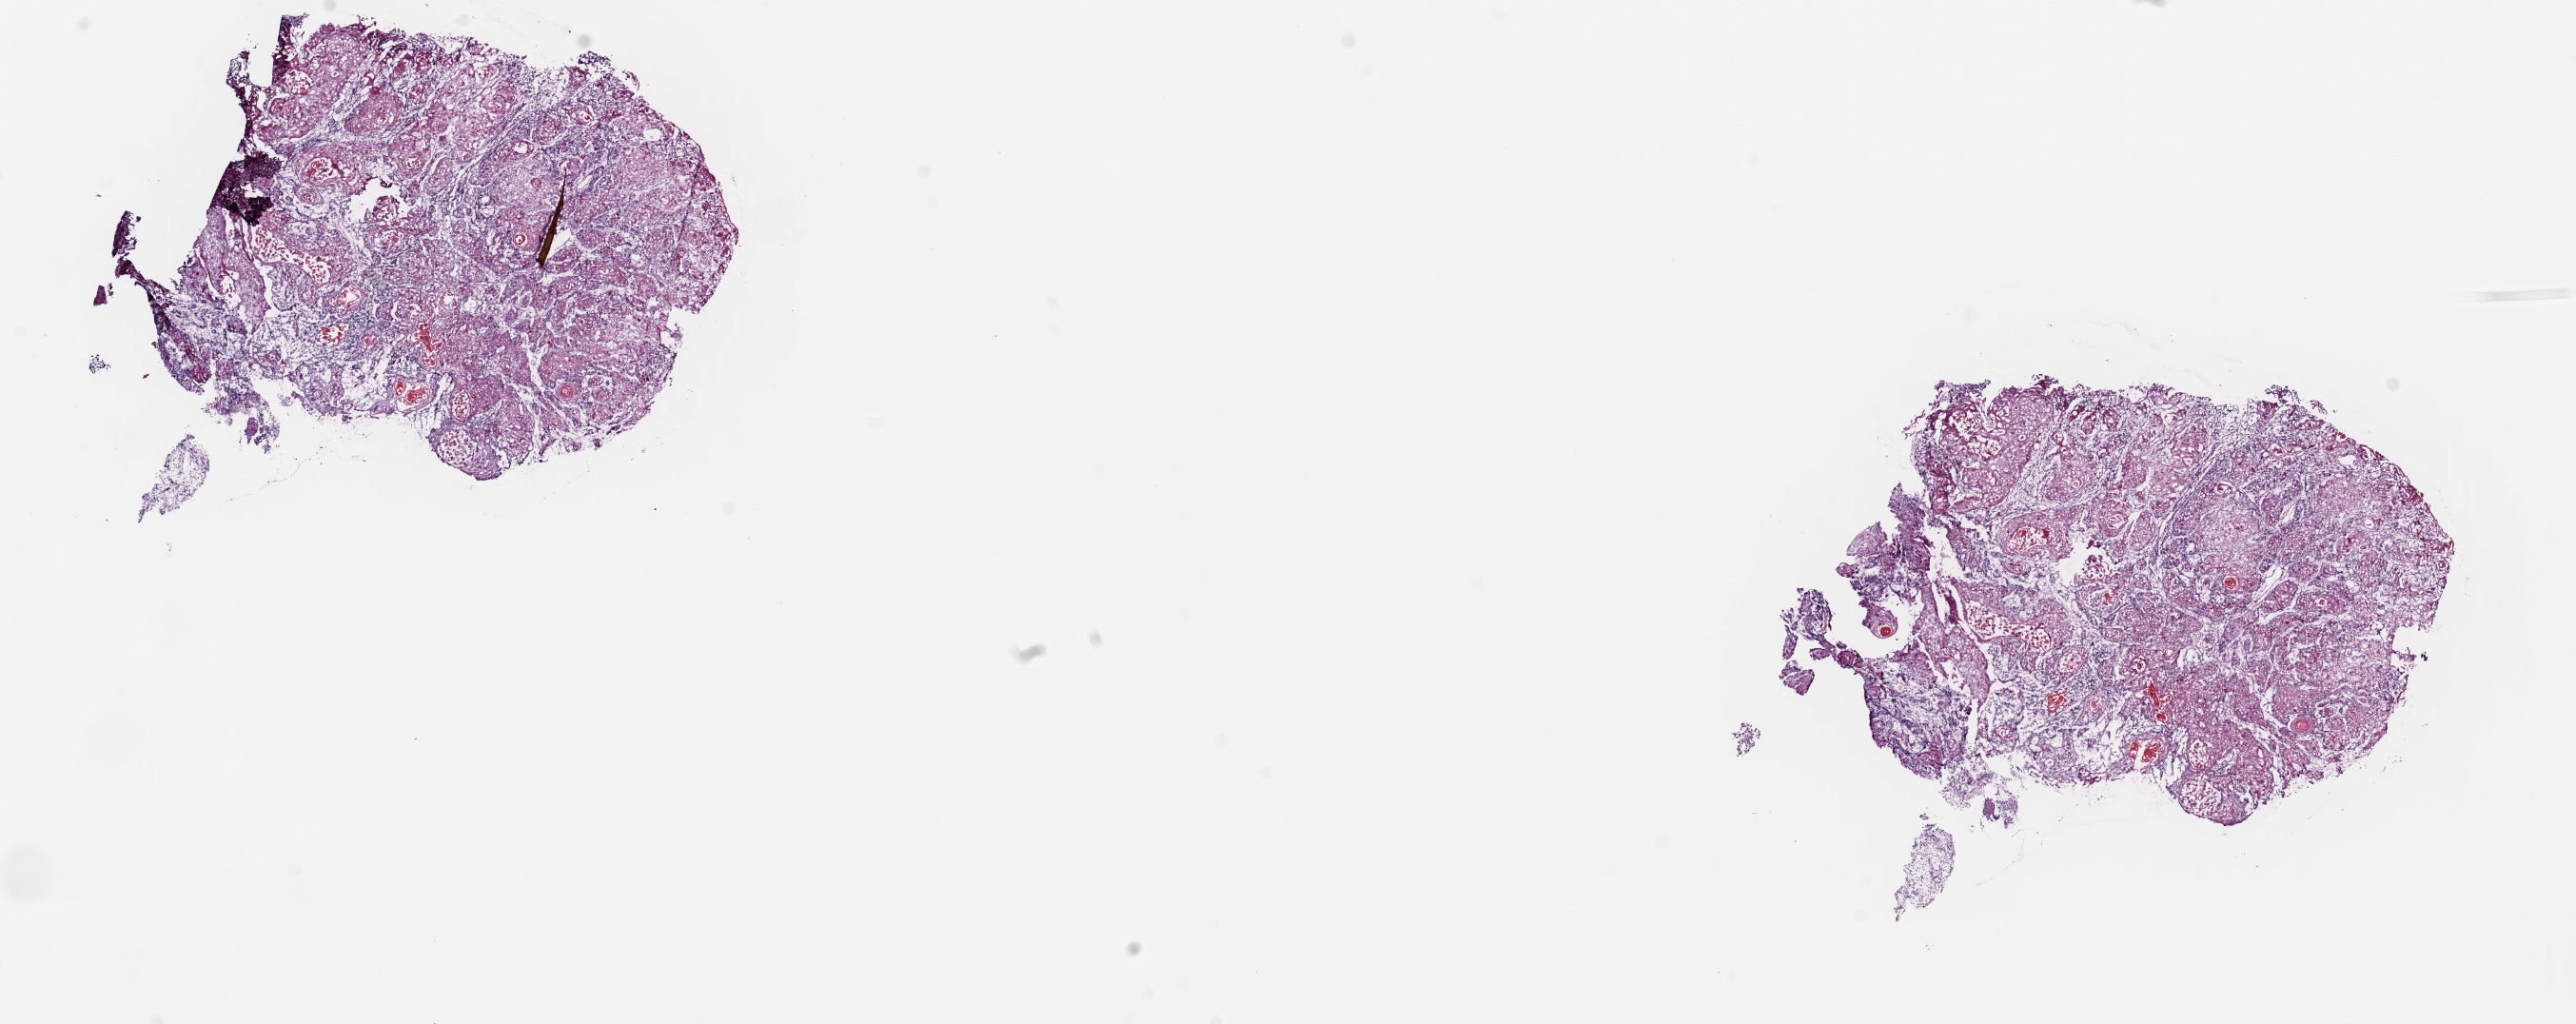
Whole-slide histology image, H&E, shown as a low-resolution overview of the whole scanned area (about 21.4 x 8.5 mm, acquisition: 40x scan), frozen section, primary tumour sample from the head and neck. Patient: male, age at initial diagnosis 54 years. Histologic grade: G2 (moderately differentiated). Pathologist review of this section (percent, as recorded): tumour cells 100%, tumour nuclei 65%, normal cells 0%, stromal cells 0%, necrosis 0%. Inflammatory infiltration, as recorded: lymphocyte infiltration 10%, monocyte infiltration 0%, neutrophil infiltration 0%.
Diagnosis: Squamous cell carcinoma, keratinizing, NOS. AJCC pathologic stage: IVA (6th edition). Laterality: left.